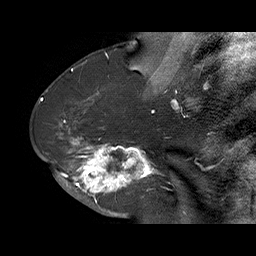
Breast MRI (dynamic contrast-enhanced), one sagittal slice; dynamic contrast-enhanced series, time point 2 of 6 at this slice position (early post-contrast); 1.5 T; TE 4.5 ms, TR 32.4 ms; 3 mm slice thickness; 256 × 256 image matrix, field of view 180 × 180 mm. Female patient. From the clinical record (not read from this slice): setting: breast cancer imaged before/during neoadjuvant chemotherapy; receptor status: HR-positive, HER2-negative.
Annotated regions visible in this slice (semi-automatic segmentation, software-assisted and operator-edited):
- analysis volume of interest (the breast-tissue region the enhancement analysis was run in; not a lesion): bounding box [x1, y1, x2, y2] px = [71, 128, 159, 202]
- tumour enhancement mask (voxels above the 100 % enhancement threshold inside the analysis volume of interest): [71, 137, 159, 202]